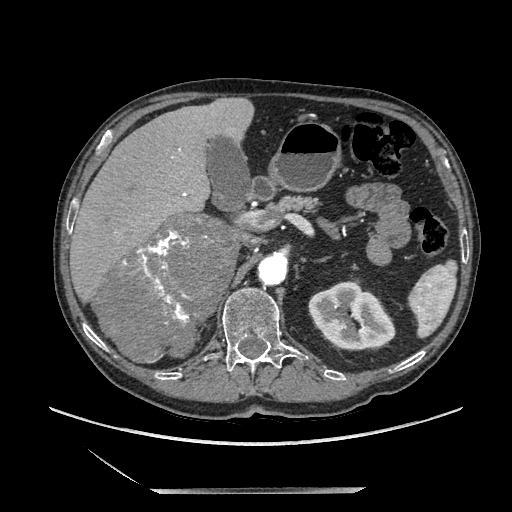
Contrast-enhanced abdominal CT, one axial slice; position 125 of 243 along the scan axis; soft-tissue window (W 400 / L 40 HU); 1.25 mm slice thickness; 512 × 512 image matrix, field of view 420 × 420 mm. Male patient. Case-level facts recorded for this patient, not image findings: diagnosis: adrenocortical carcinoma; tumour side: right adrenal; tumour size at pathology: 16 cm; Ki-67 index: 17 %; stage (as recorded): 3.
Outlined on this slice (semi-automatically segmented with operator editing):
- mass: bounding box [x1, y1, x2, y2] px = [98, 214, 239, 362]